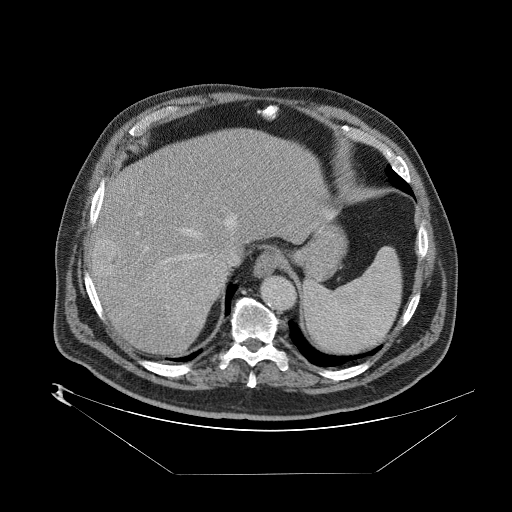
Contrast-enhanced abdominal CT (liver protocol), one axial slice; position 65 of 89 along the scan axis; one of 2 acquisitions stored at this slice position; soft-tissue window (W 400 / L 40 HU); 2.5 mm slice thickness; 512 × 512 image matrix, field of view 480 × 480 mm. Case-level facts recorded for this patient, not image findings: diagnosis: hepatocellular carcinoma (patient treated with transarterial chemoembolisation; whether this scan precedes or follows treatment is not stated here); TNM stage (as recorded): Stage-II; Child-Pugh class: B; tumour differentiation: moderately differentiated; tumour nodularity: multinodular.
Outlined on this slice (semi-automatically segmented with operator editing):
- abdominal aorta: bounding box <261,278,295,311> (left, top, right, bottom; pixels)
- liver parenchyma outside the tumour (the mass and vessels are separate outlines, so this box may not span the whole liver): <90,126,332,352>
- mass: <99,243,220,321>
- liver vessels: <96,210,219,316>